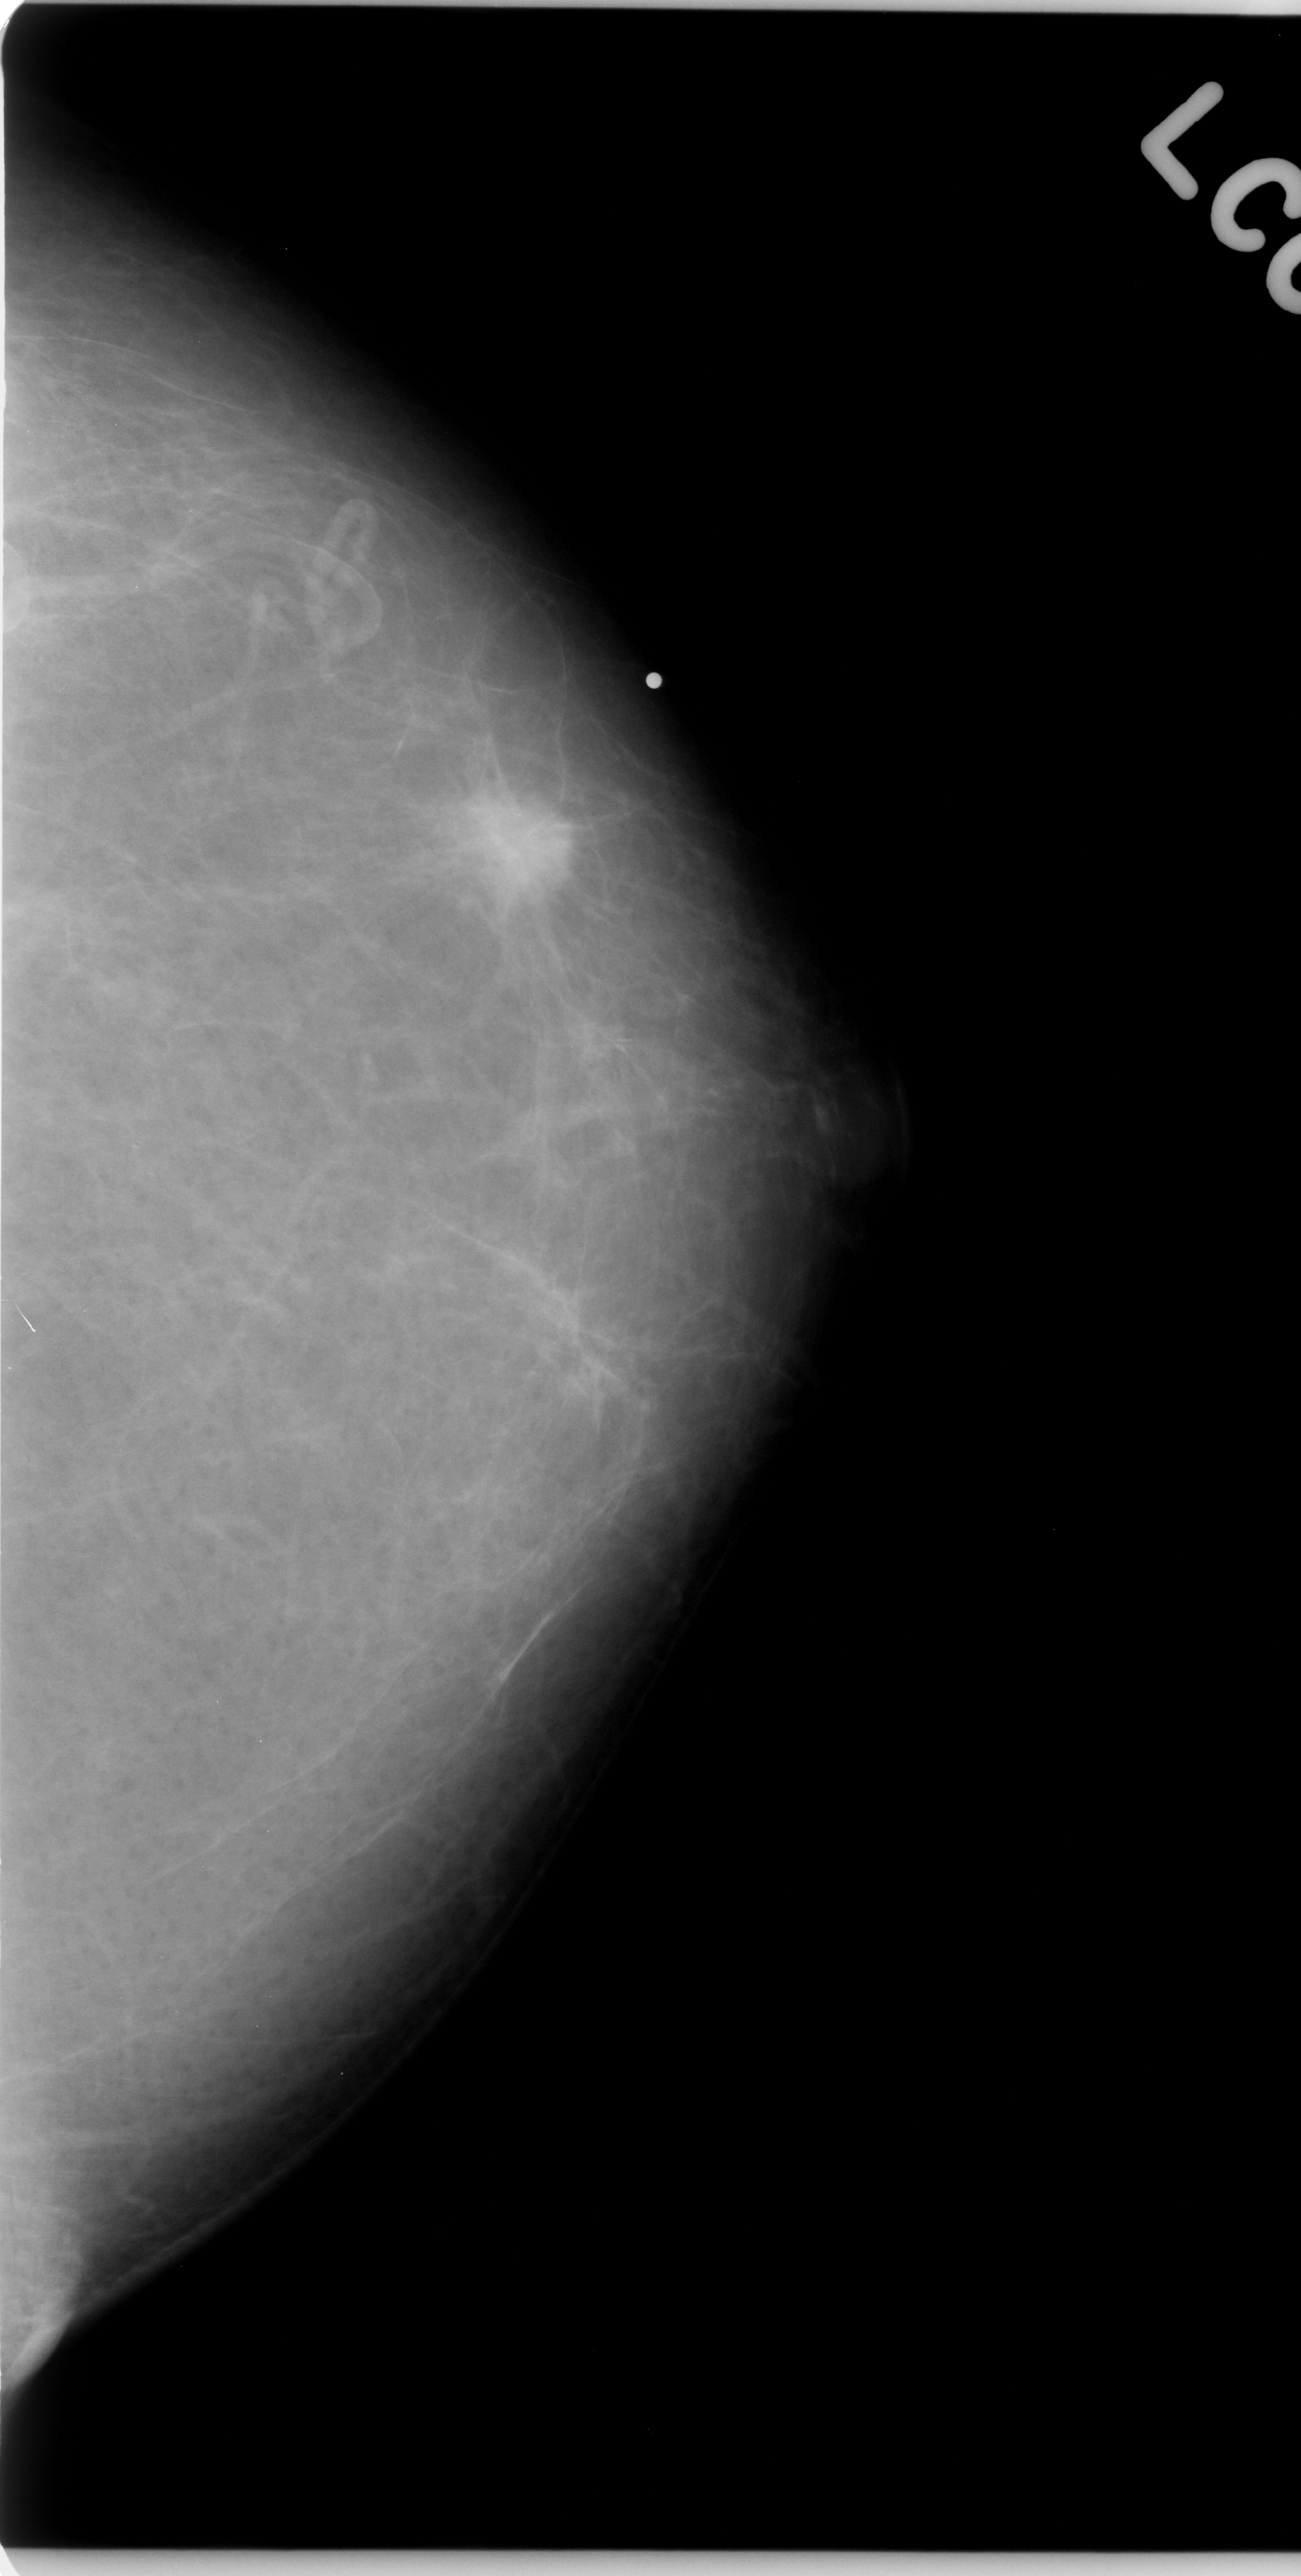
Mammogram (digitized film); left breast; CC view; BI-RADS breast density category 1 (scale 1–4); 1301 × 2576 image matrix.
Expert-marked regions of interest on this film, with their recorded descriptors:
- mass, shape irregular, margins spiculated; BI-RADS assessment category 5; subtlety rating 5 on a 1 (subtle) to 5 (obvious) scale; pathology (as recorded): malignant: bounding box <436,746,605,939> (left, top, right, bottom; pixels)